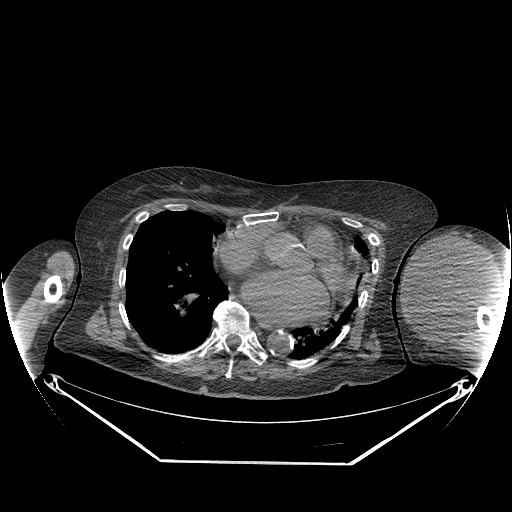
CT of an extremity soft-tissue mass (from a PET/CT study), one axial slice. Position 162 of 267 along the scan axis. Soft-tissue window (W 400 / L 40 HU). 512 × 512 image matrix, field of view 500 × 500 mm. Female patient. From the clinical record (not read from this slice): histological type: pleiomorphic leiomyosarcoma; grade: high; site of the primary tumour: left biceps.
Outlined on this slice (expert contour drawn on MRI and transferred to this co-registered scan by the dataset authors):
- gross tumour volume including surrounding oedema: bounding box [x1, y1, x2, y2] px = [402, 235, 490, 330]
- gross tumour volume (mass): [402, 235, 490, 330]